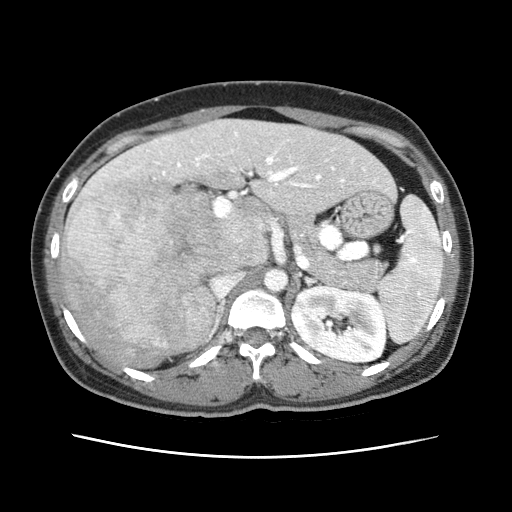
Contrast-enhanced abdominal CT (liver protocol), one axial slice; slice 33 of 79 in the series (ordered by position); reconstruction kernel STANDARD; soft-tissue window (W 400 / L 40 HU); 2.5 mm slice thickness; 512 × 512 image matrix, field of view 340 × 340 mm. Case-level facts recorded for this patient, not image findings: diagnosis: hepatocellular carcinoma (patient treated with transarterial chemoembolisation; whether this scan precedes or follows treatment is not stated here); TNM stage (as recorded): Stage-I; Child-Pugh class: A; tumour nodularity: uninodular.
Structures marked on this image (semi-automatically segmented with operator editing):
- abdominal aorta: bounding box <264,268,287,291> (left, top, right, bottom; pixels)
- liver parenchyma outside the tumour (the mass and vessels are separate outlines, so this box may not span the whole liver): <60,118,394,366>
- mass: <60,176,227,365>
- liver vessels: <102,132,365,218>